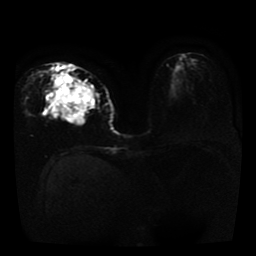
Breast MRI, one axial slice; position 16 of 41 along the scan axis; diffusion-weighted series; image 2 of 4 stored at this slice position (different b-values; order by instance number); 1.5 T; 5 mm slice thickness; 256 × 256 image matrix, field of view 330 × 330 mm. Female patient.
Structures marked on this image (manually delineated by an expert):
- tumour on diffusion-weighted imaging: bounding box <49,74,93,125> (left, top, right, bottom; pixels)